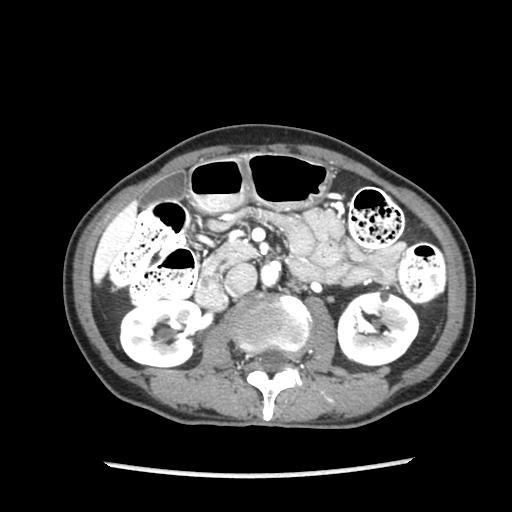
Contrast-enhanced abdominal CT (liver protocol), one axial slice; slice 36 of 87 in the series (ordered by position); soft-tissue window (W 400 / L 40 HU); 512 × 512 image matrix. From the clinical record (not read from this slice): diagnosis: hepatocellular carcinoma (patient treated with transarterial chemoembolisation; whether this scan precedes or follows treatment is not stated here); TNM stage (as recorded): Stage-IIIB; Child-Pugh class: A; tumour nodularity: uninodular.
Outlined on this slice (semi-automatically segmented with operator editing):
- liver parenchyma outside the tumour (the mass and vessels are separate outlines, so this box may not span the whole liver): bounding box (x1, y1, x2, y2) in pixels: (94, 200, 137, 284)
- liver vessels: (98, 223, 129, 263)